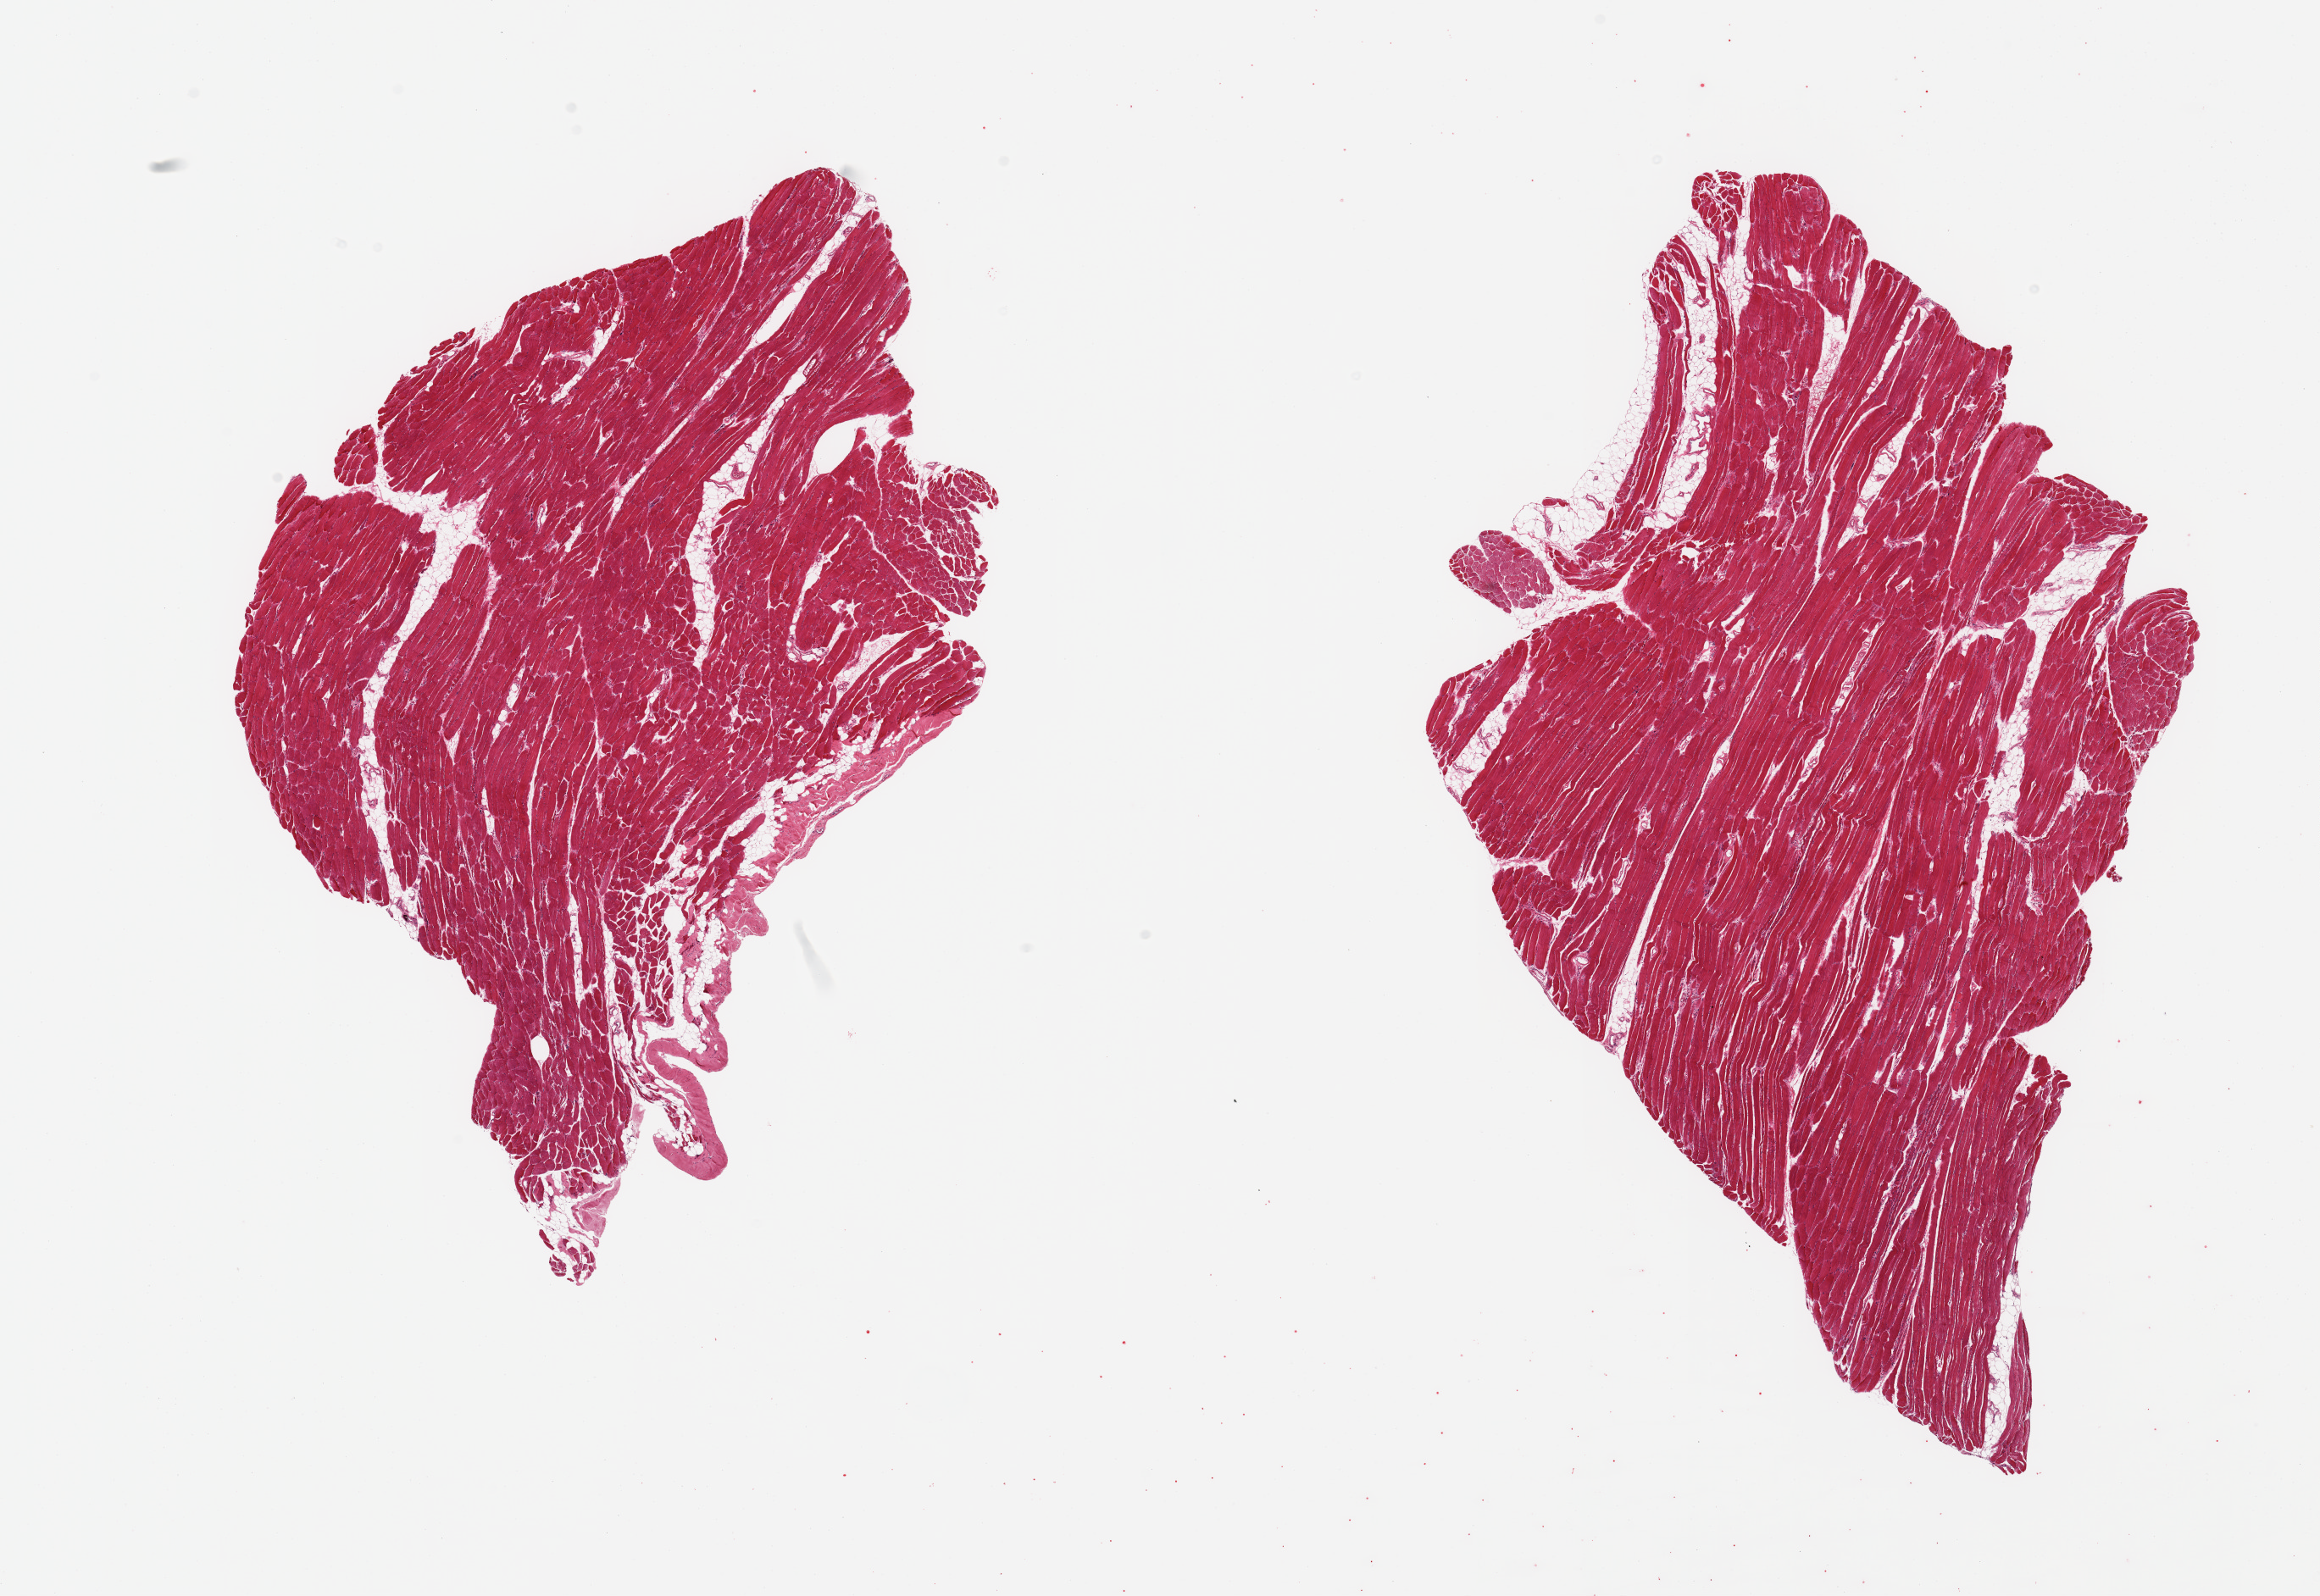
Whole-slide image, hematoxylin and eosin (H&E) stain, shown as a low-resolution overview of the whole scanned area (about 21.7 x 14.9 mm, from a 20x scan). PAXgene-fixed, paraffin-embedded tissue. Target tissue: skeletal muscle. Tissue donor sample. Male donor.
Reviewer comment on this tissue sample: 2 pieces; focal atrophy; 10% internal fat.